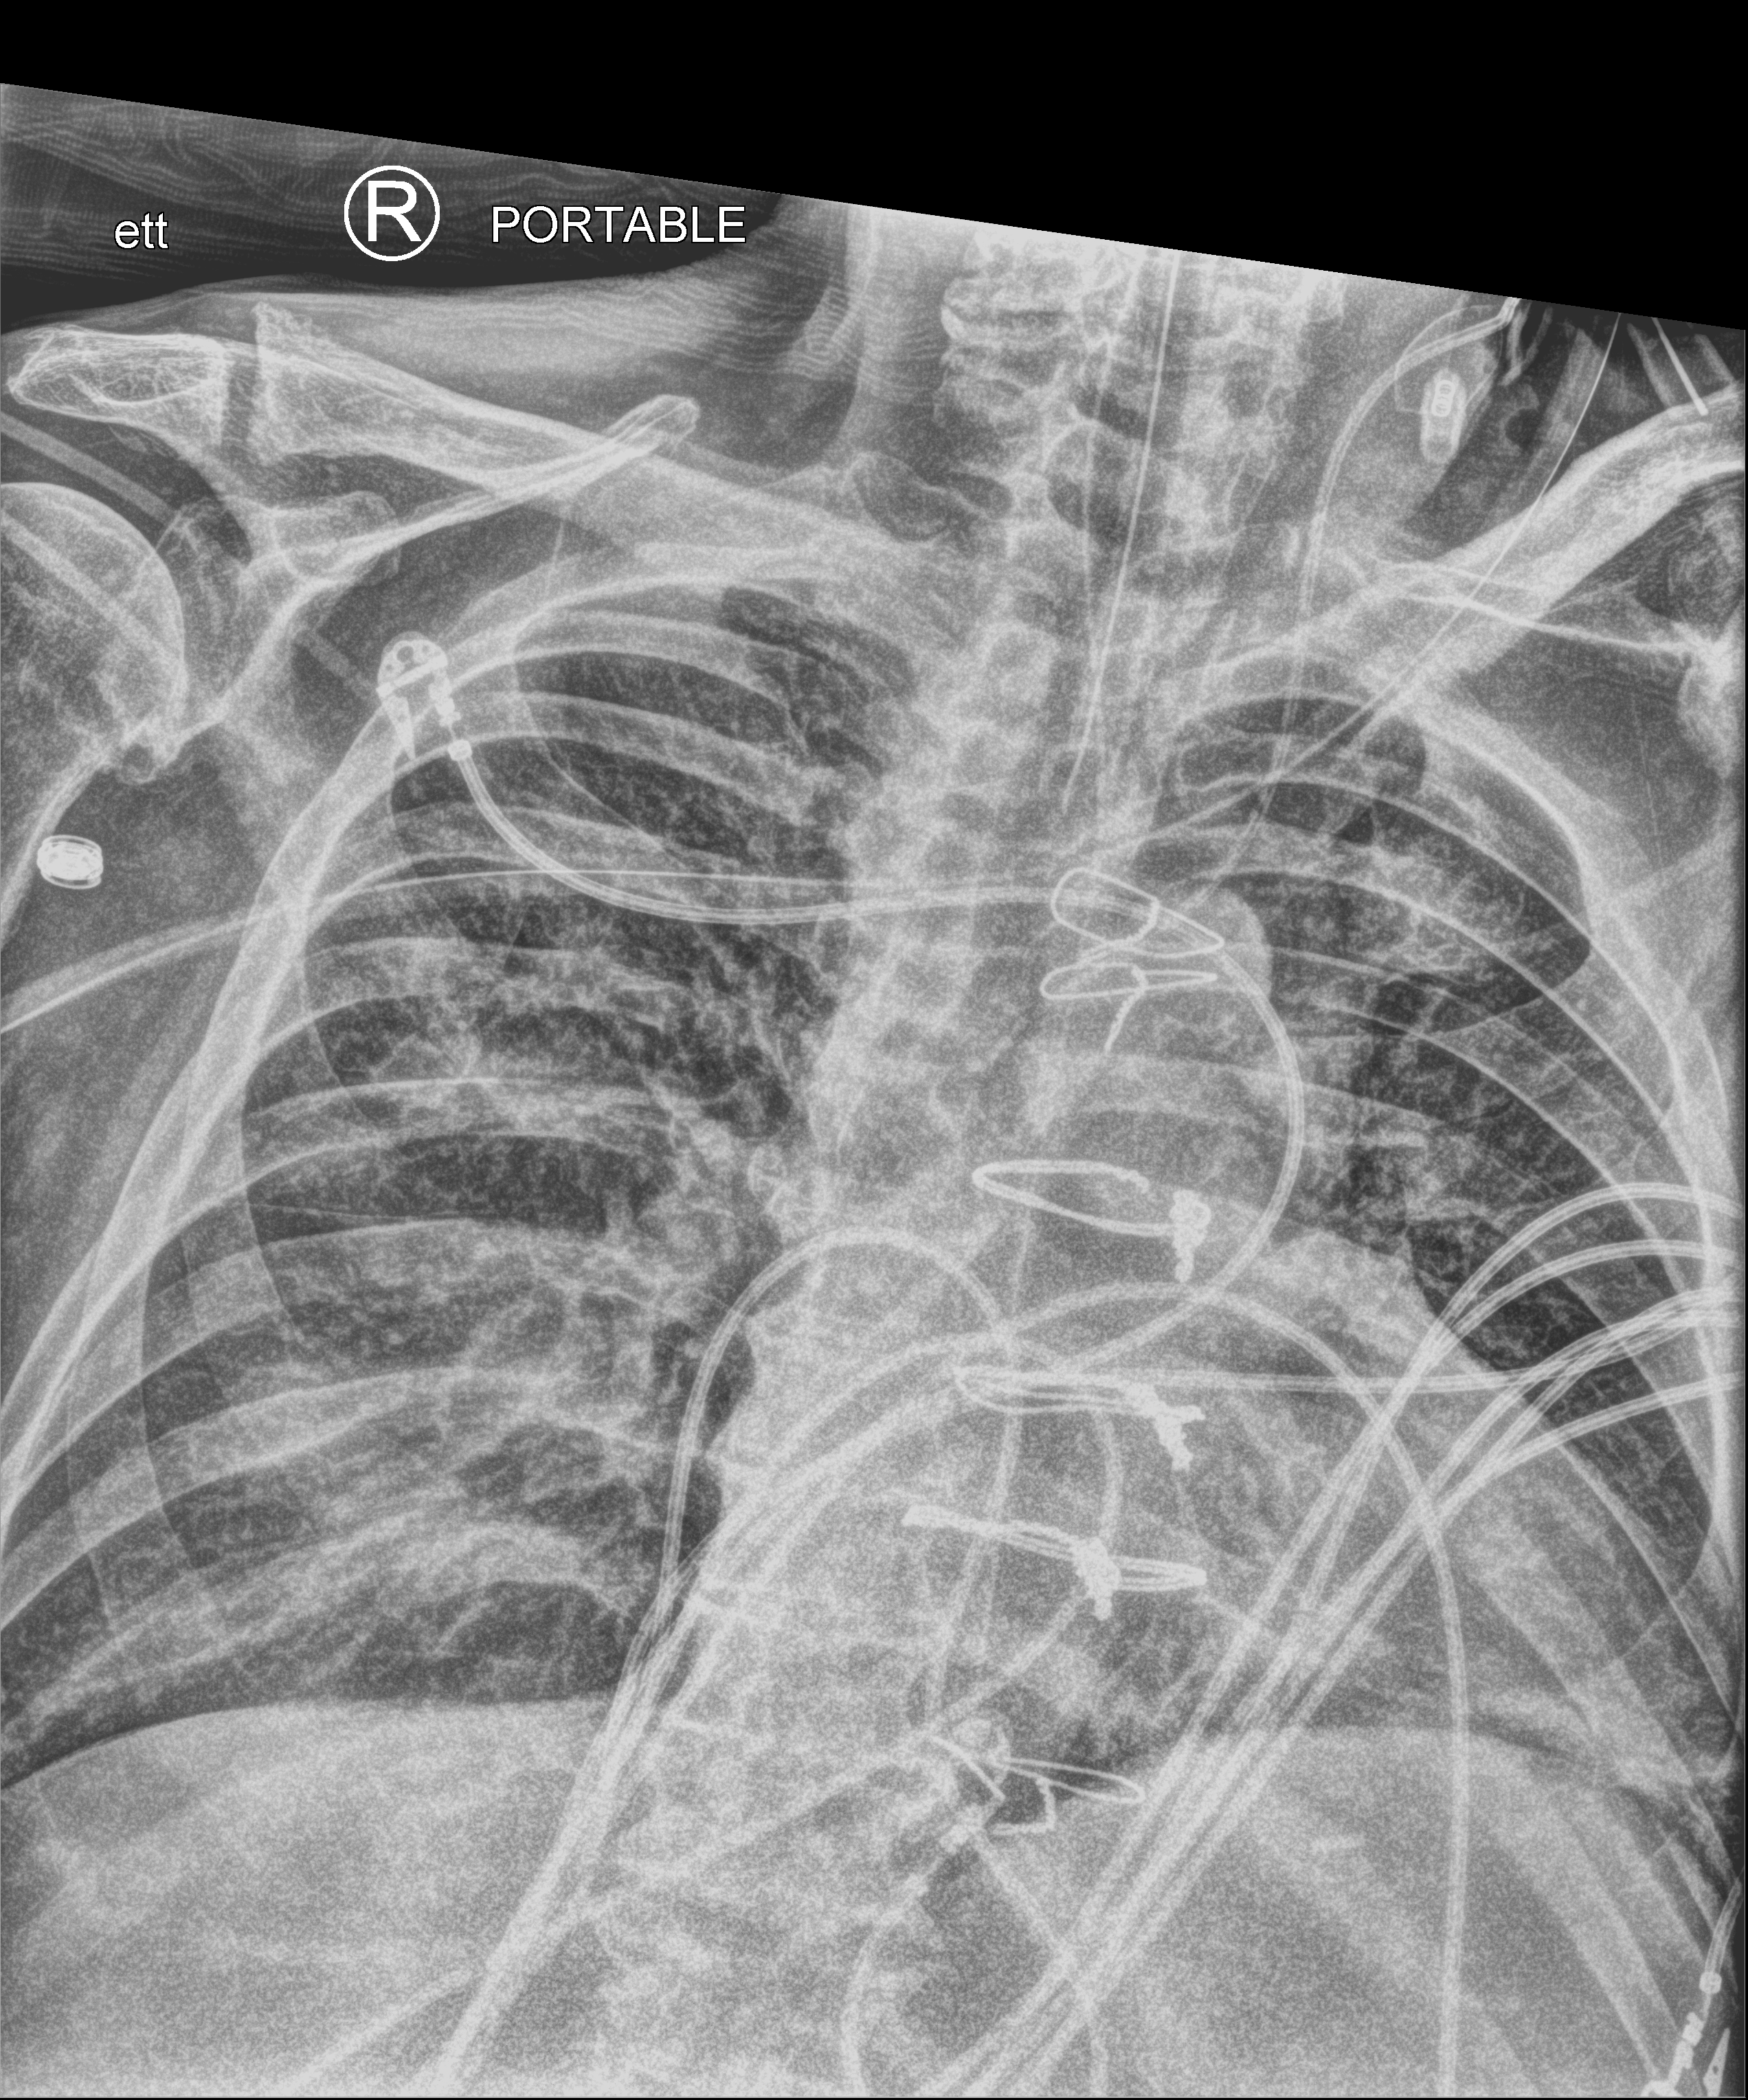
Bedside chest radiograph (computed radiography). Patient hospitalised with COVID-19; male, aged 60–74 years.
Hospital-stay facts (about this admission, not read from this image; timing relative to this image not recorded): admitted to intensive care during this hospital stay: yes; other chronic lung disease (admission record): no; chronic kidney disease (admission record): yes.